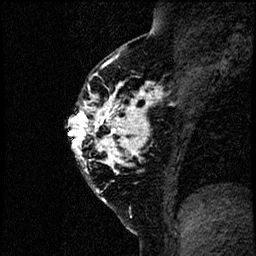
Breast MRI (dynamic contrast-enhanced), one sagittal slice. Position 41 of 60 along the scan axis. Dynamic contrast-enhanced study with each time point stored as its own series, time point 2 of 4 at this slice position (early post-contrast, ordered by acquisition time). 1.5 T. TE 4.2 ms, TR 17.6 ms. 2 mm slice thickness. 256 × 256 image matrix, field of view 200 × 200 mm. Female patient, age 40 years. From the clinical record (not read from this slice): setting: breast cancer imaged before/during neoadjuvant chemotherapy; receptor status: HER2-positive.
Outlined on this slice (semi-automatically segmented with operator editing):
- analysis volume of interest (the breast-tissue region the enhancement analysis was run in; not a lesion): bounding box <66,55,185,206> (left, top, right, bottom; pixels)
- tumour enhancement mask (voxels above the 100 % enhancement threshold inside the analysis volume of interest): <67,58,148,167>